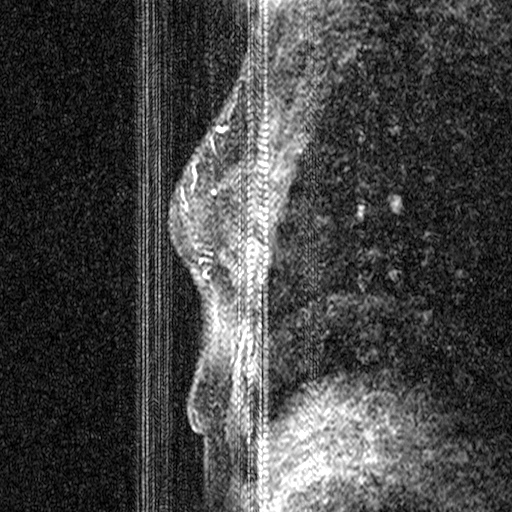
Breast MRI (dynamic contrast-enhanced), one sagittal slice; position 21 of 44 along the scan axis; dynamic contrast-enhanced study with each time point stored as its own series, time point 2 of 3 at this slice position (early post-contrast, ordered by acquisition time); 1.5 T; TE 4.5 ms, TR 11 ms; 512 × 512 image matrix, field of view 200 × 200 mm. Female patient, age 44 years. Case-level facts recorded for this patient, not image findings: setting: breast cancer imaged before/during neoadjuvant chemotherapy; receptor status: HR-positive, HER2-negative.
Annotated regions visible in this slice (semi-automatically segmented with operator editing):
- analysis volume of interest (the breast-tissue region the enhancement analysis was run in; not a lesion): bounding box <206,164,245,299> (left, top, right, bottom; pixels)
- tumour enhancement mask (voxels above the 90 % enhancement threshold inside the analysis volume of interest): <206,253,212,262>